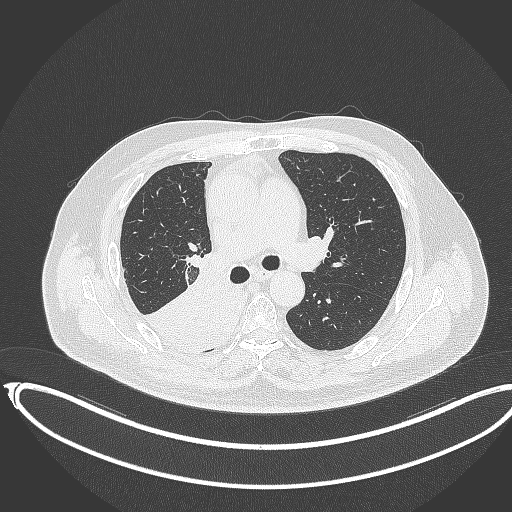
Chest CT, one axial slice. Slice 220 of 403 in the series (ordered by position). Reconstruction kernel B70f. 120 kVp. Lung window (W 1500 / L -600 HU). 512 × 512 image matrix, field of view 436 × 436 mm. Male patient, age 68 years. From the clinical record (not read from this slice): clinical TNM (as recorded): T2a N0 M0.
Annotated regions visible in this slice (bounding box drawn by a radiologist):
- lung tumour (recorded histology: adenocarcinoma): bounding box [x1, y1, x2, y2] px = [149, 268, 246, 349]